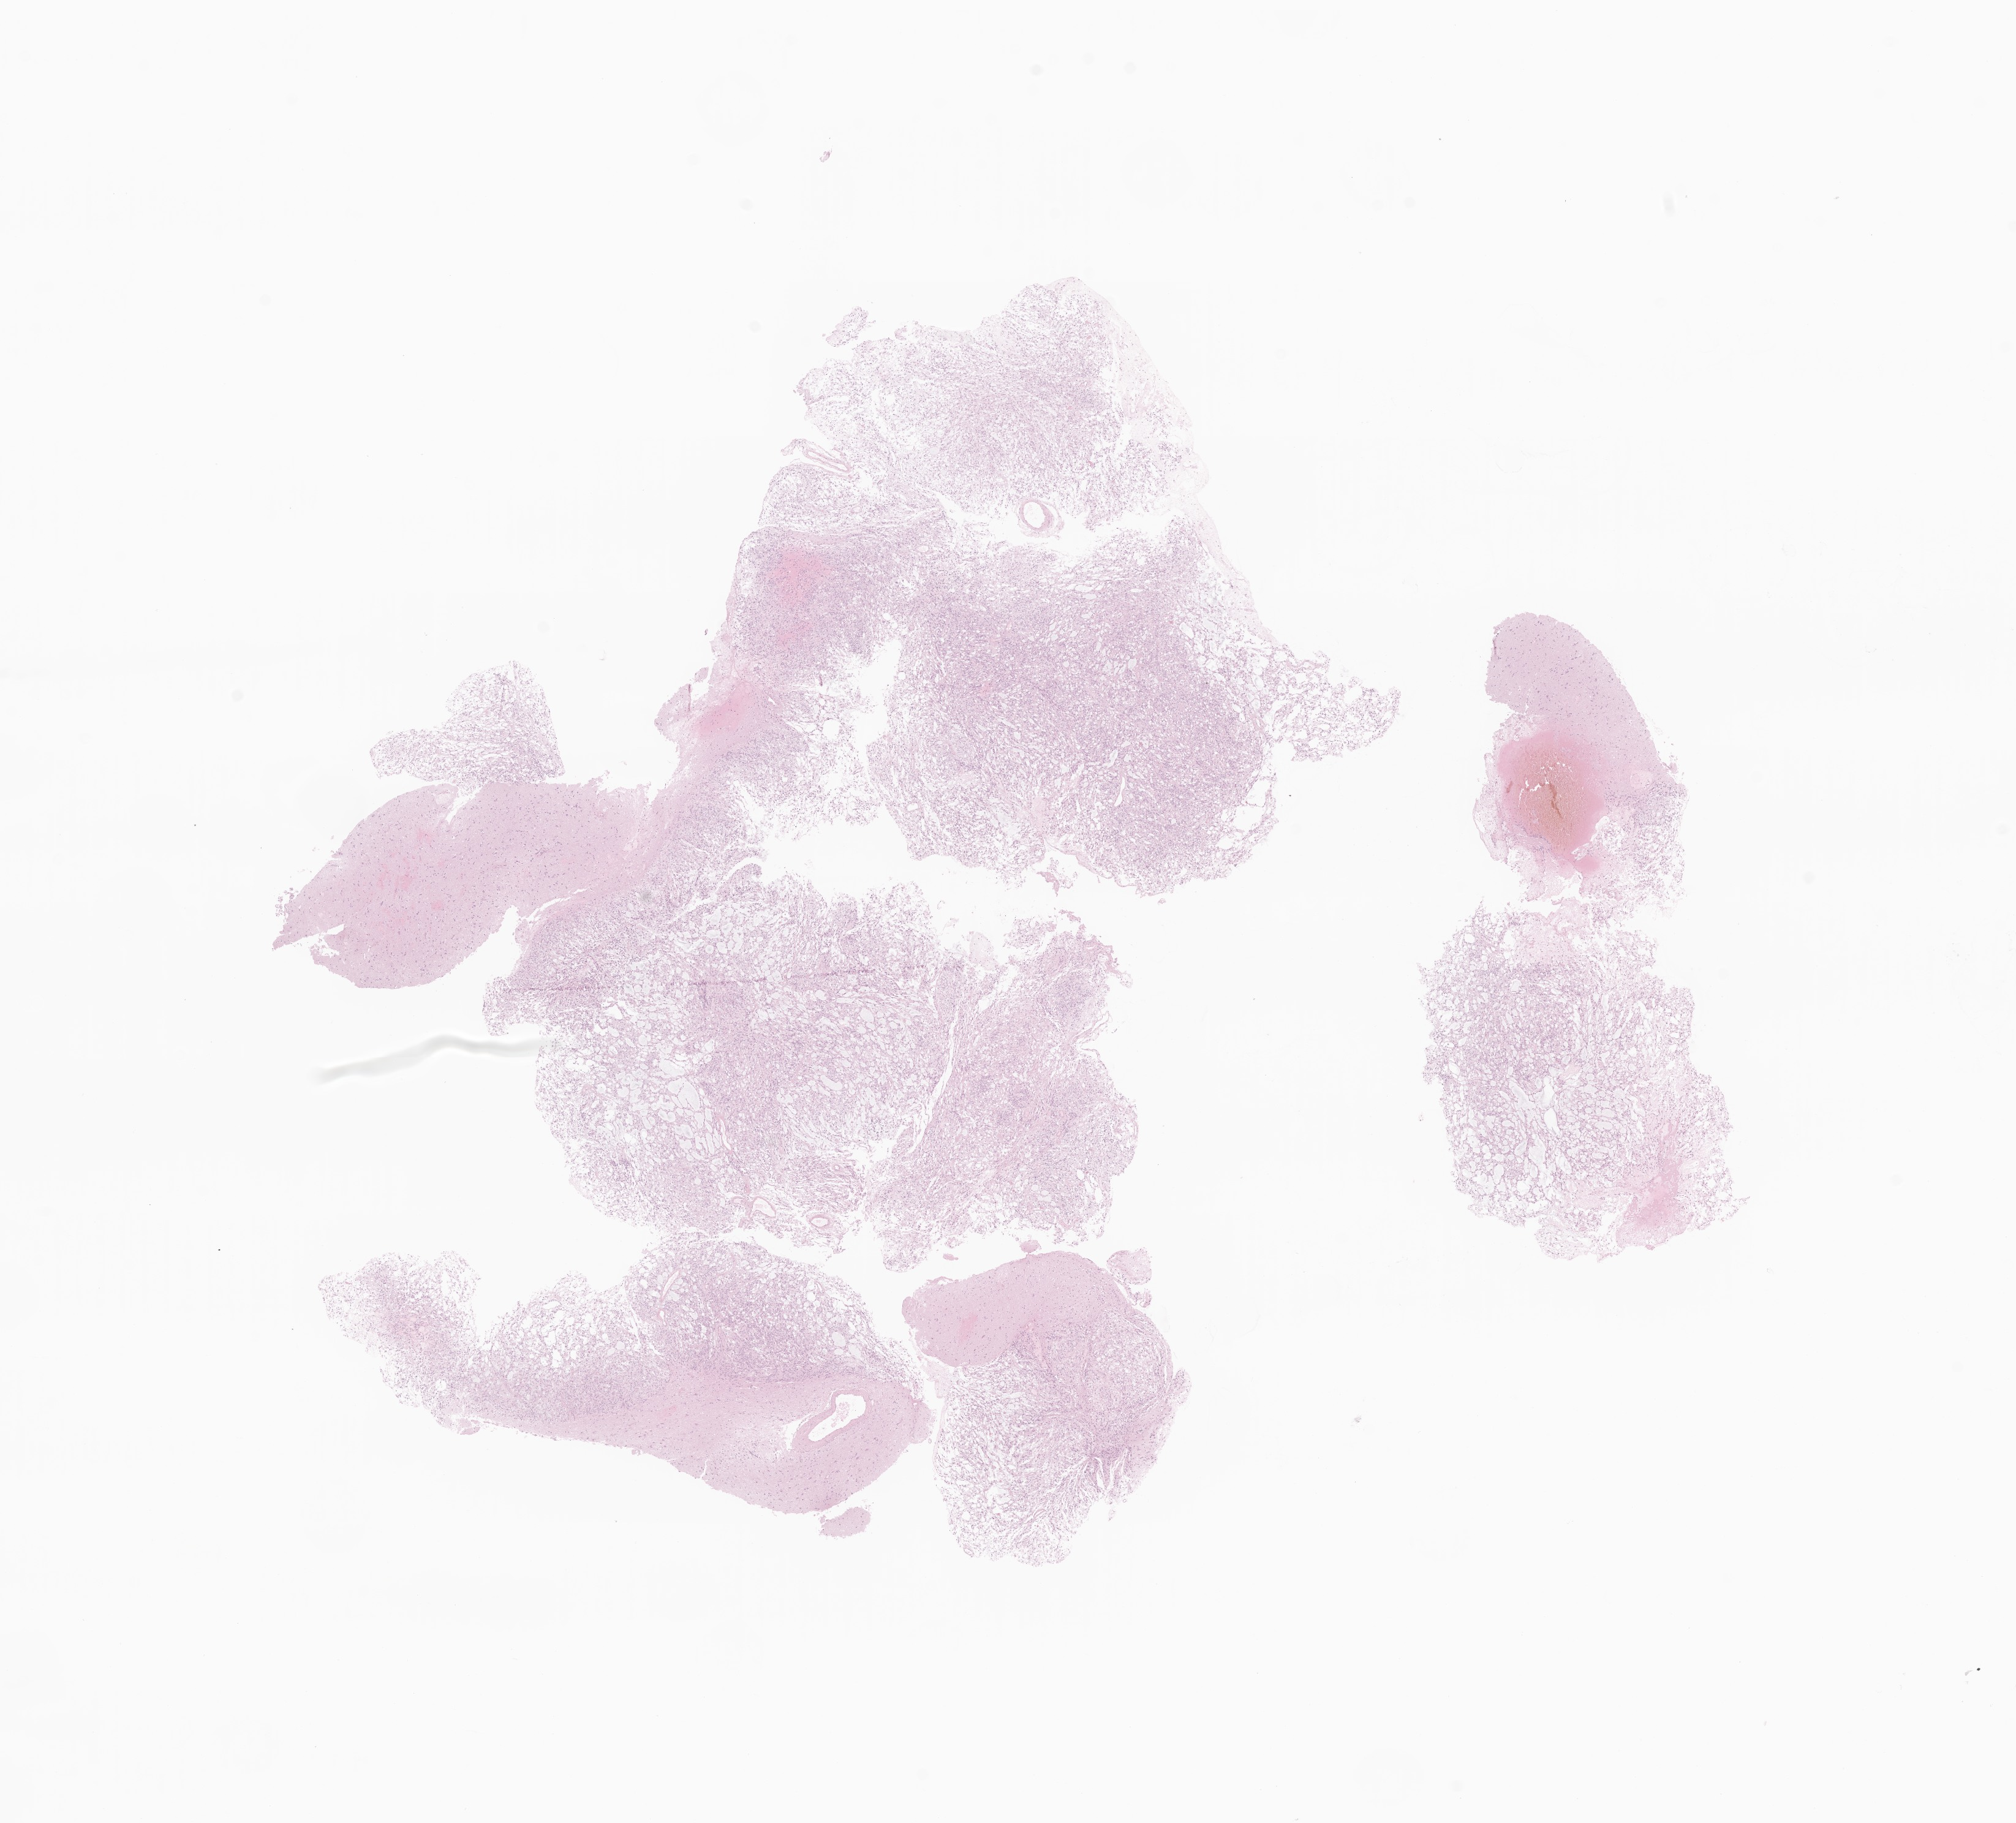
Whole-slide image, H&E stain of tumor tissue from the occipital lobe — a low-resolution overview of the entire scanned area, about 13.9 x 12.5 mm. Formalin-fixed paraffin-embedded section. Female patient, age 172 months (14 years 4 months).
Diagnosis: Ependymoma, NOS.